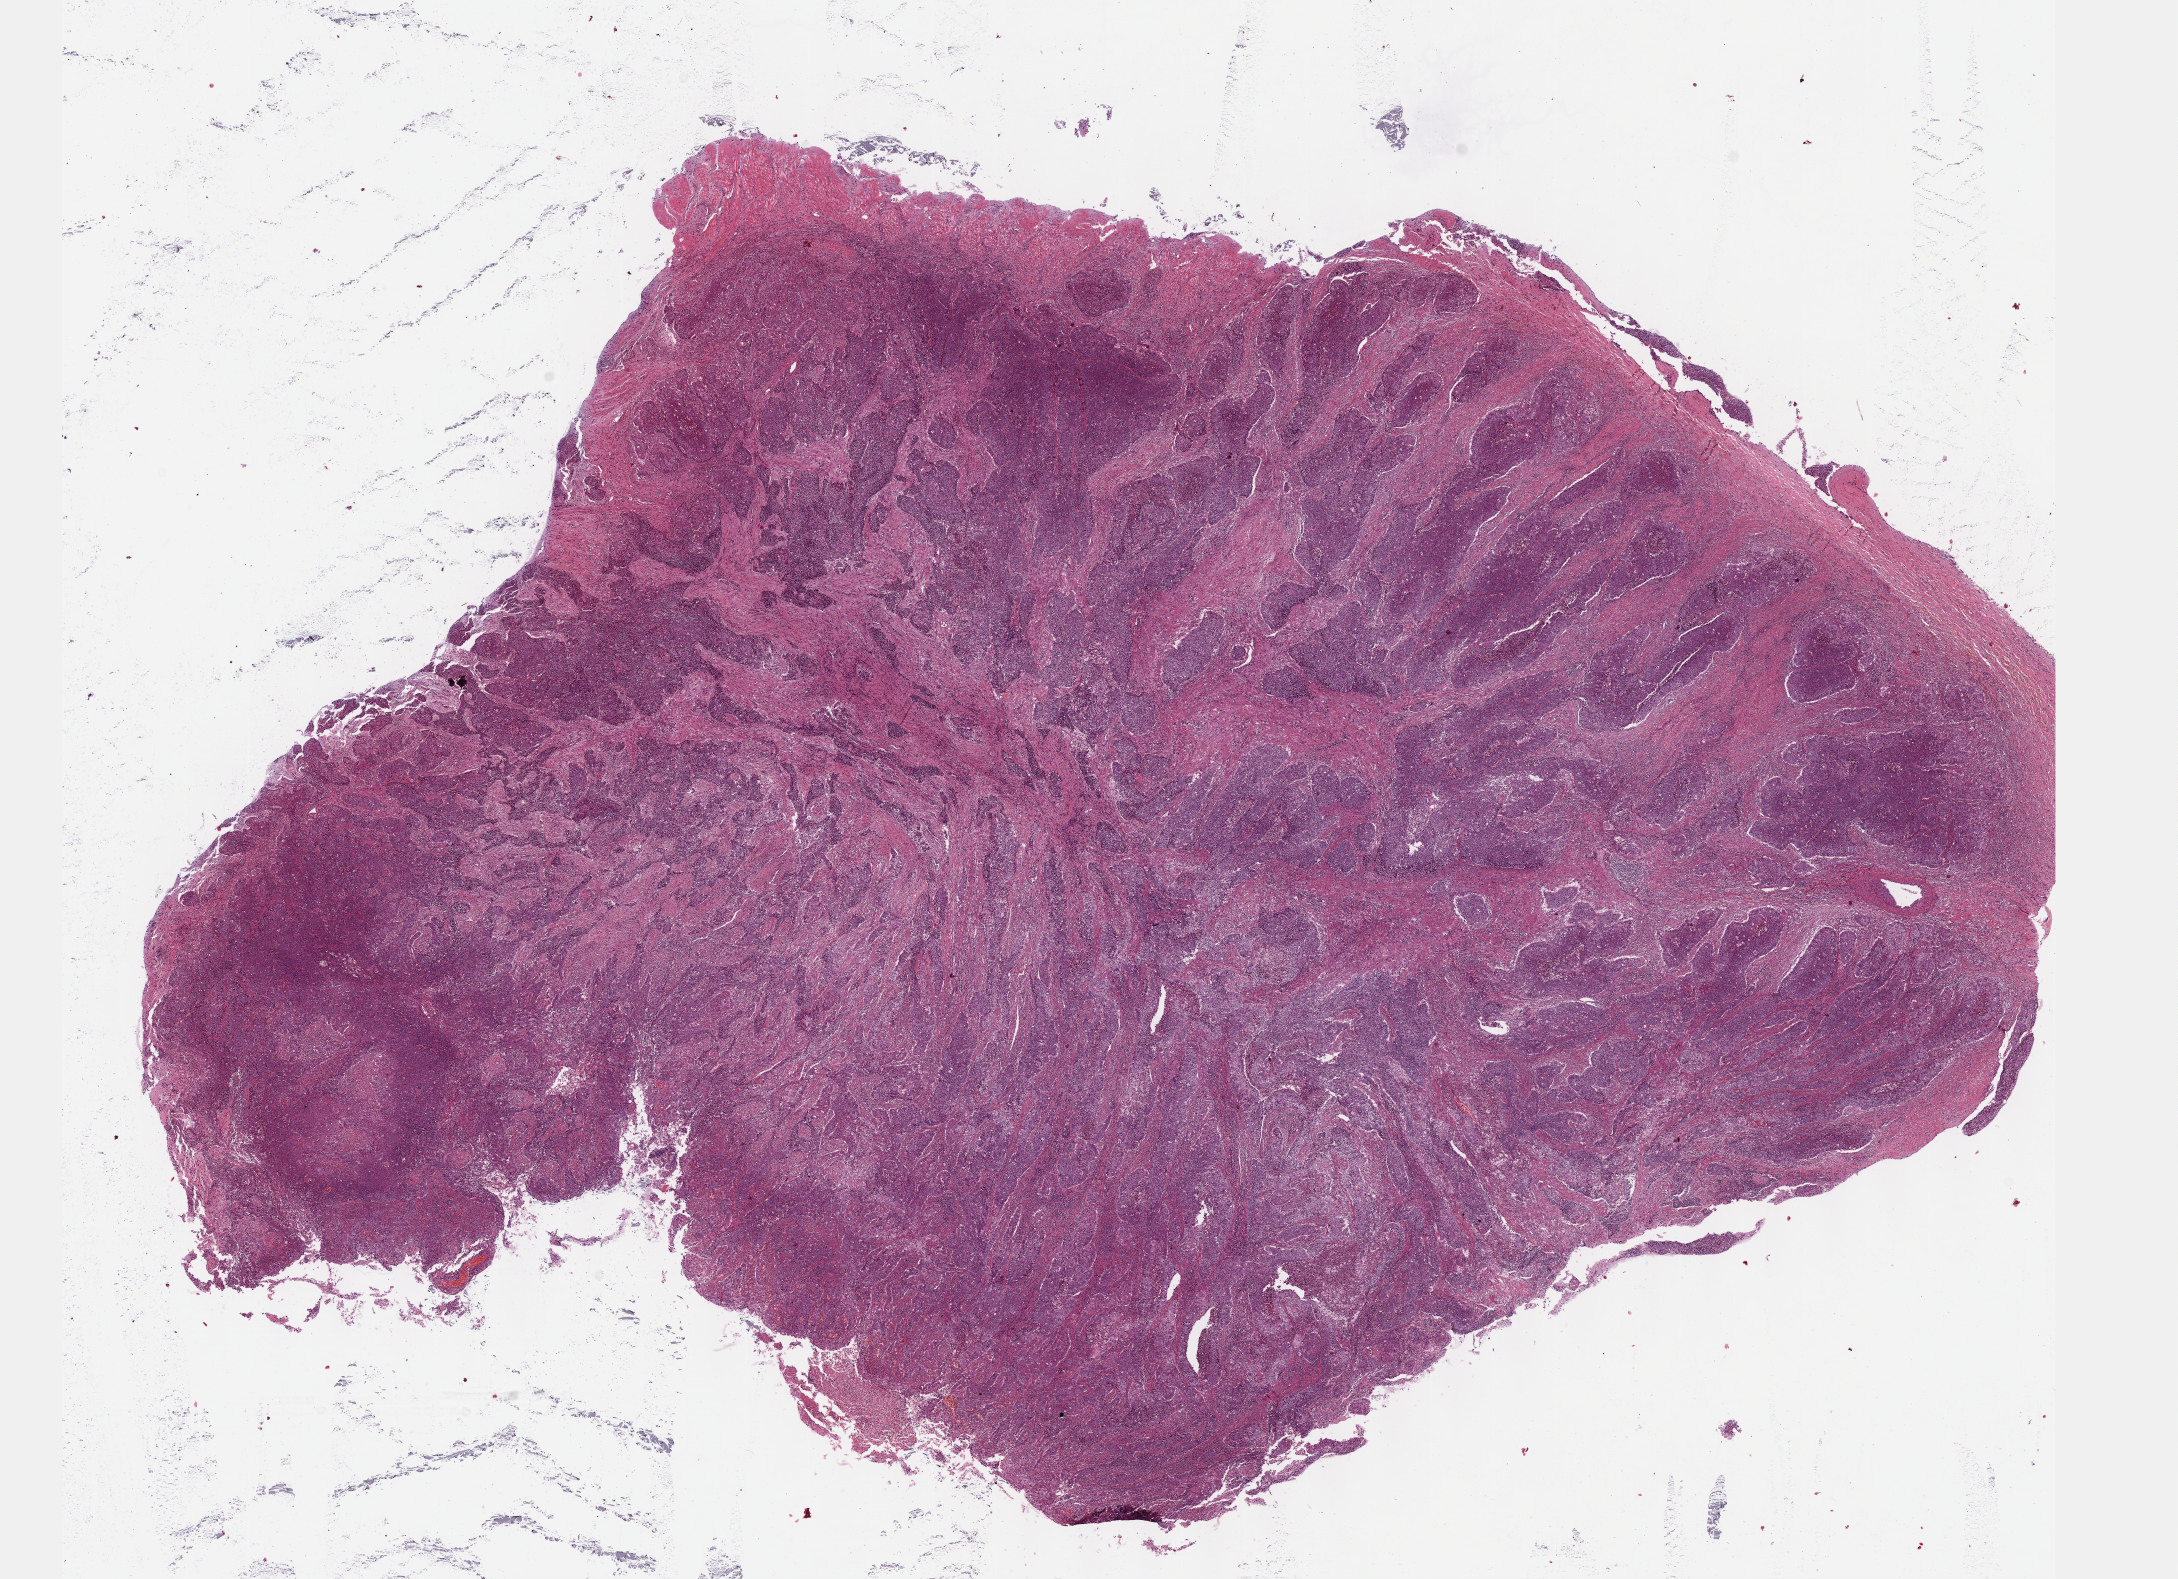
Whole-slide histology image, Hematoxylin and eosin (H&E) stained — a low-resolution overview of the entire scanned area, about 17.6 x 12.8 mm (from a 40x scan). Formalin-fixed paraffin-embedded (FFPE) diagnostic section. Esophagus, primary tumour sample. Patient: female, age at initial diagnosis 67 years. Histologic grade: G3 (poorly differentiated).
AJCC pathologic stage: IIA (6th edition). TNM: T2 N0 M0. Histologic diagnosis: Squamous cell carcinoma, NOS.